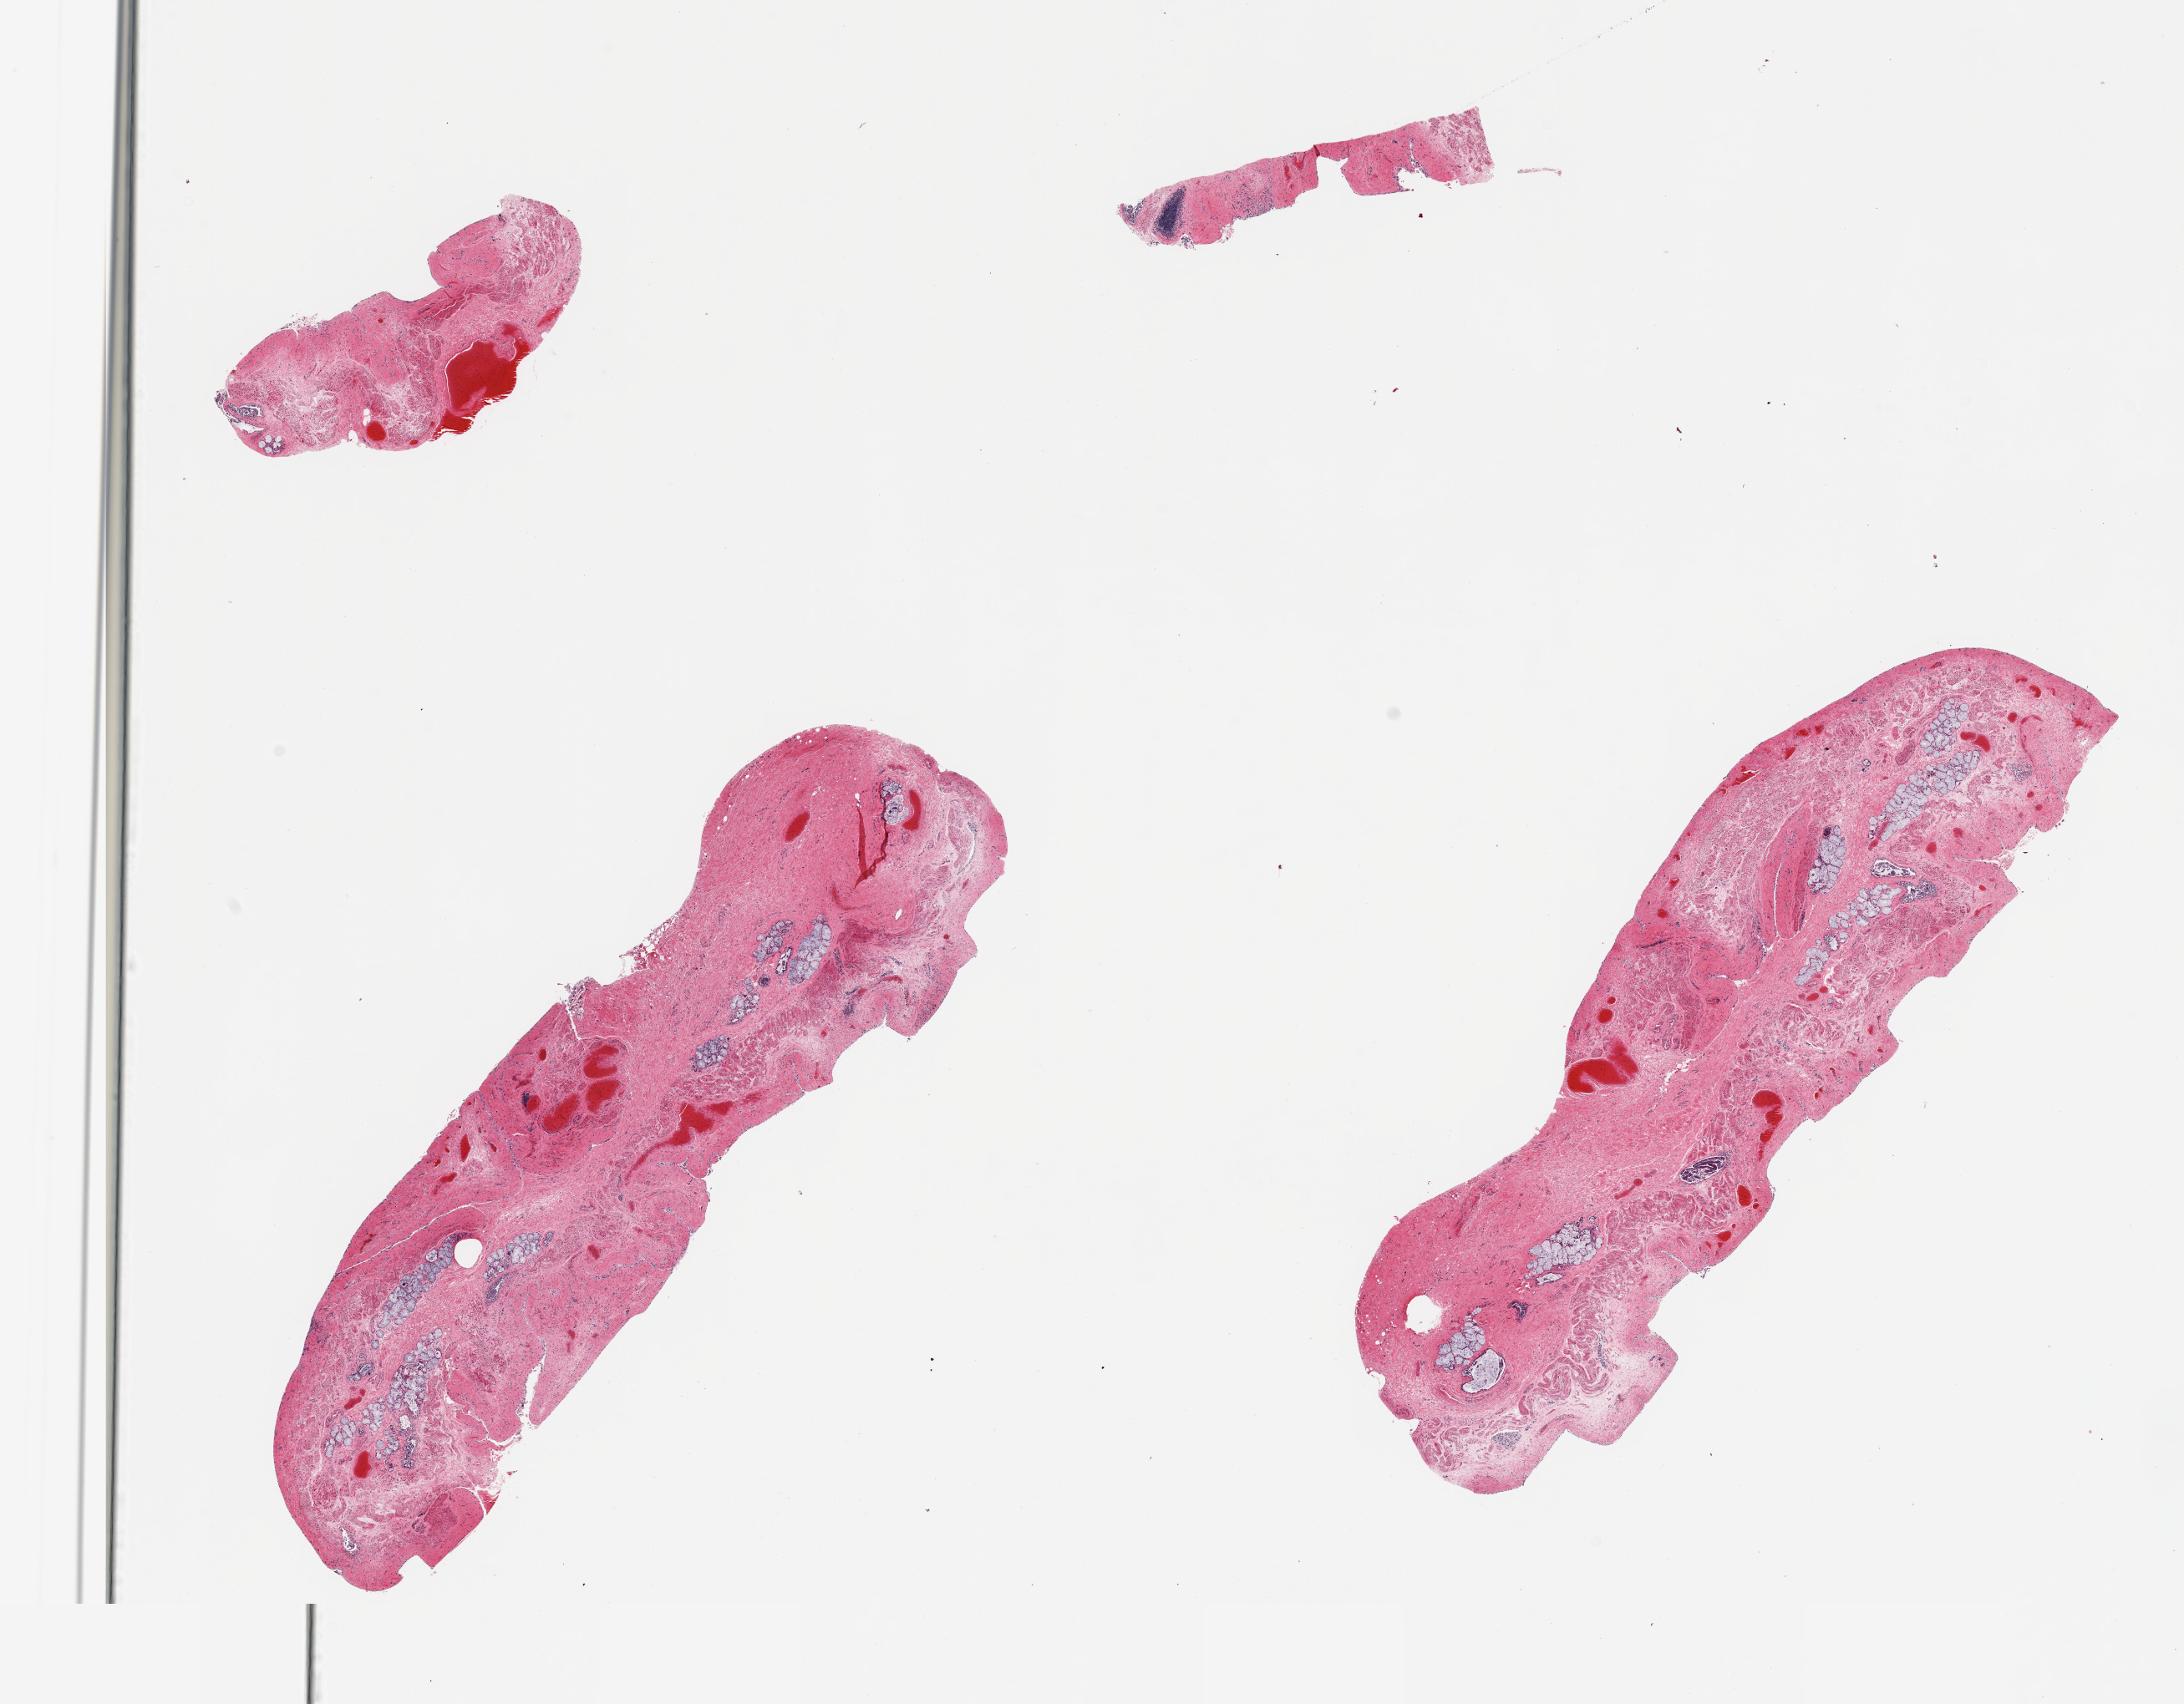
Haematoxylin and eosin whole-slide image, whole scanned area (about 20.7 x 16.1 mm) shown as a low-resolution overview; PAXgene-fixed, paraffin-embedded tissue; section of esophageal mucous membrane (target tissue); donor tissue sample. Donor: female.
* reviewer comment on this tissue sample: 4 pieces; mucosa sloughed; submucosal glands and stroma remain